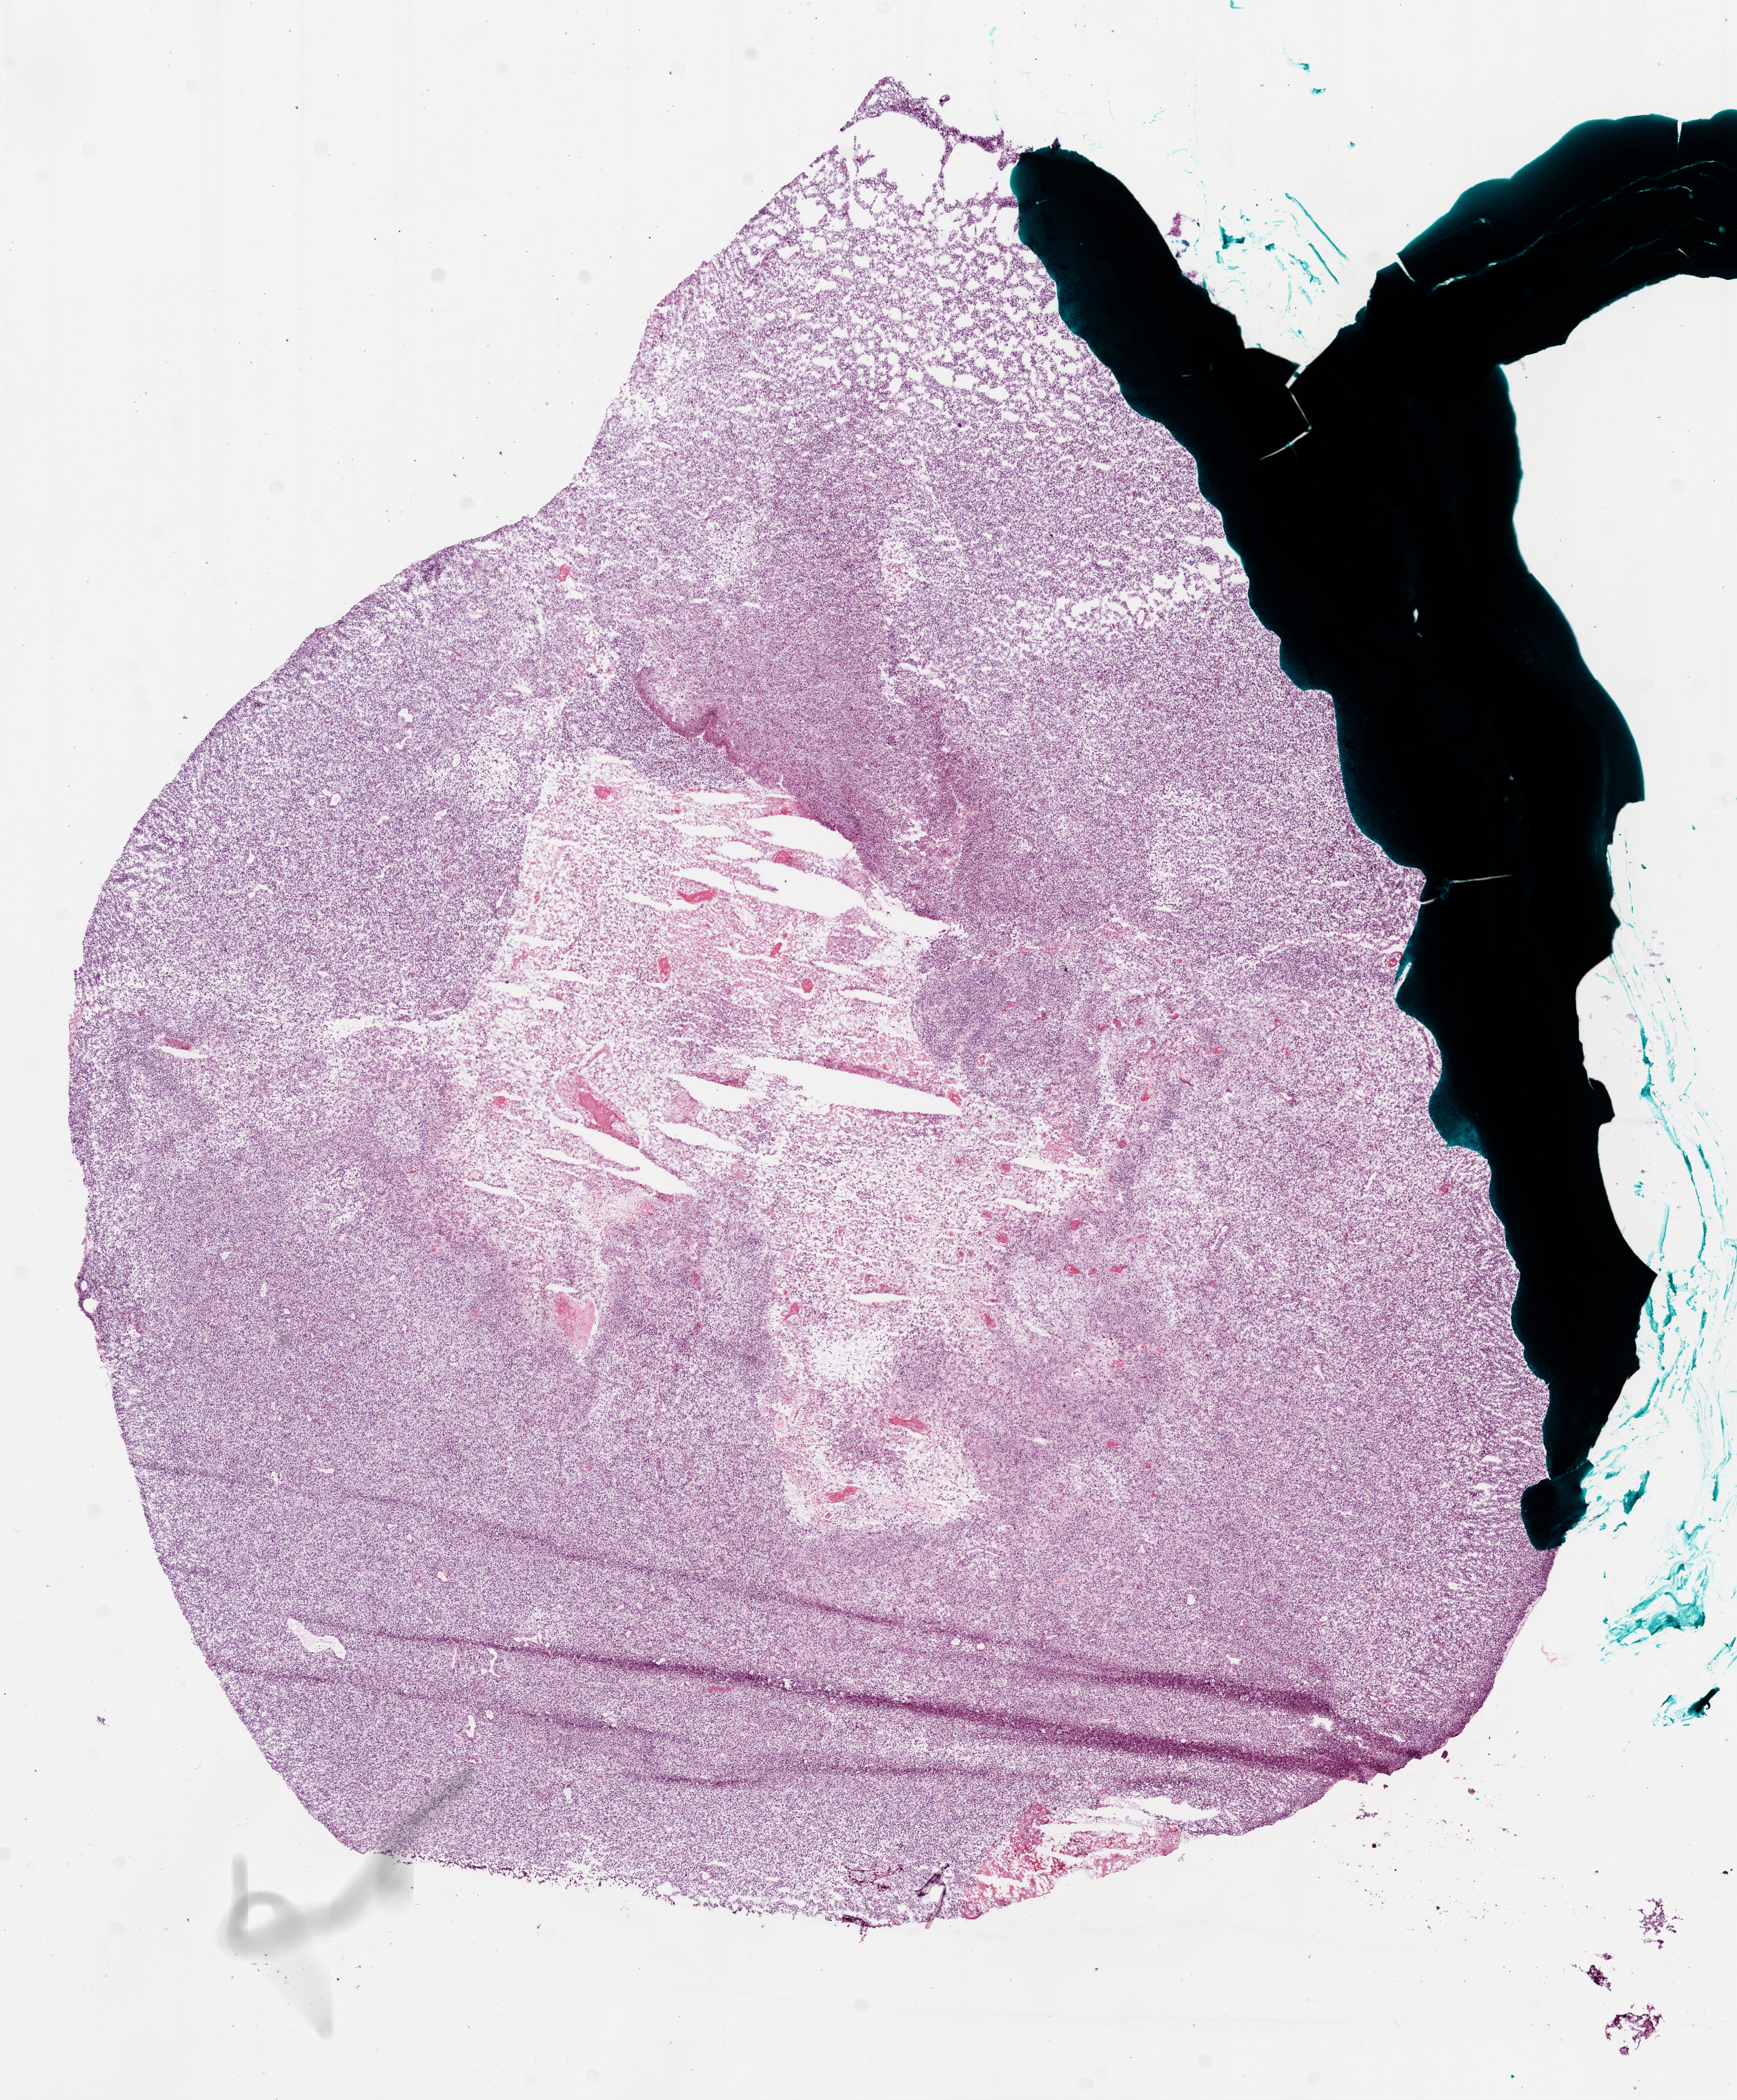
Whole-slide histology image, H&E-stained — low-resolution overview of the scanned area, about 10.2 x 12.3 mm (acquisition: 20x scan). Frozen section. Sample: primary tumour, brain. Male patient; age at initial diagnosis 65 years. Slide review estimates, as recorded: tumour cells 70%, tumour nuclei 95%, necrosis 30%. Infiltration values recorded for this section: neutrophil infiltration 100%.
Diagnosis: Glioblastoma.